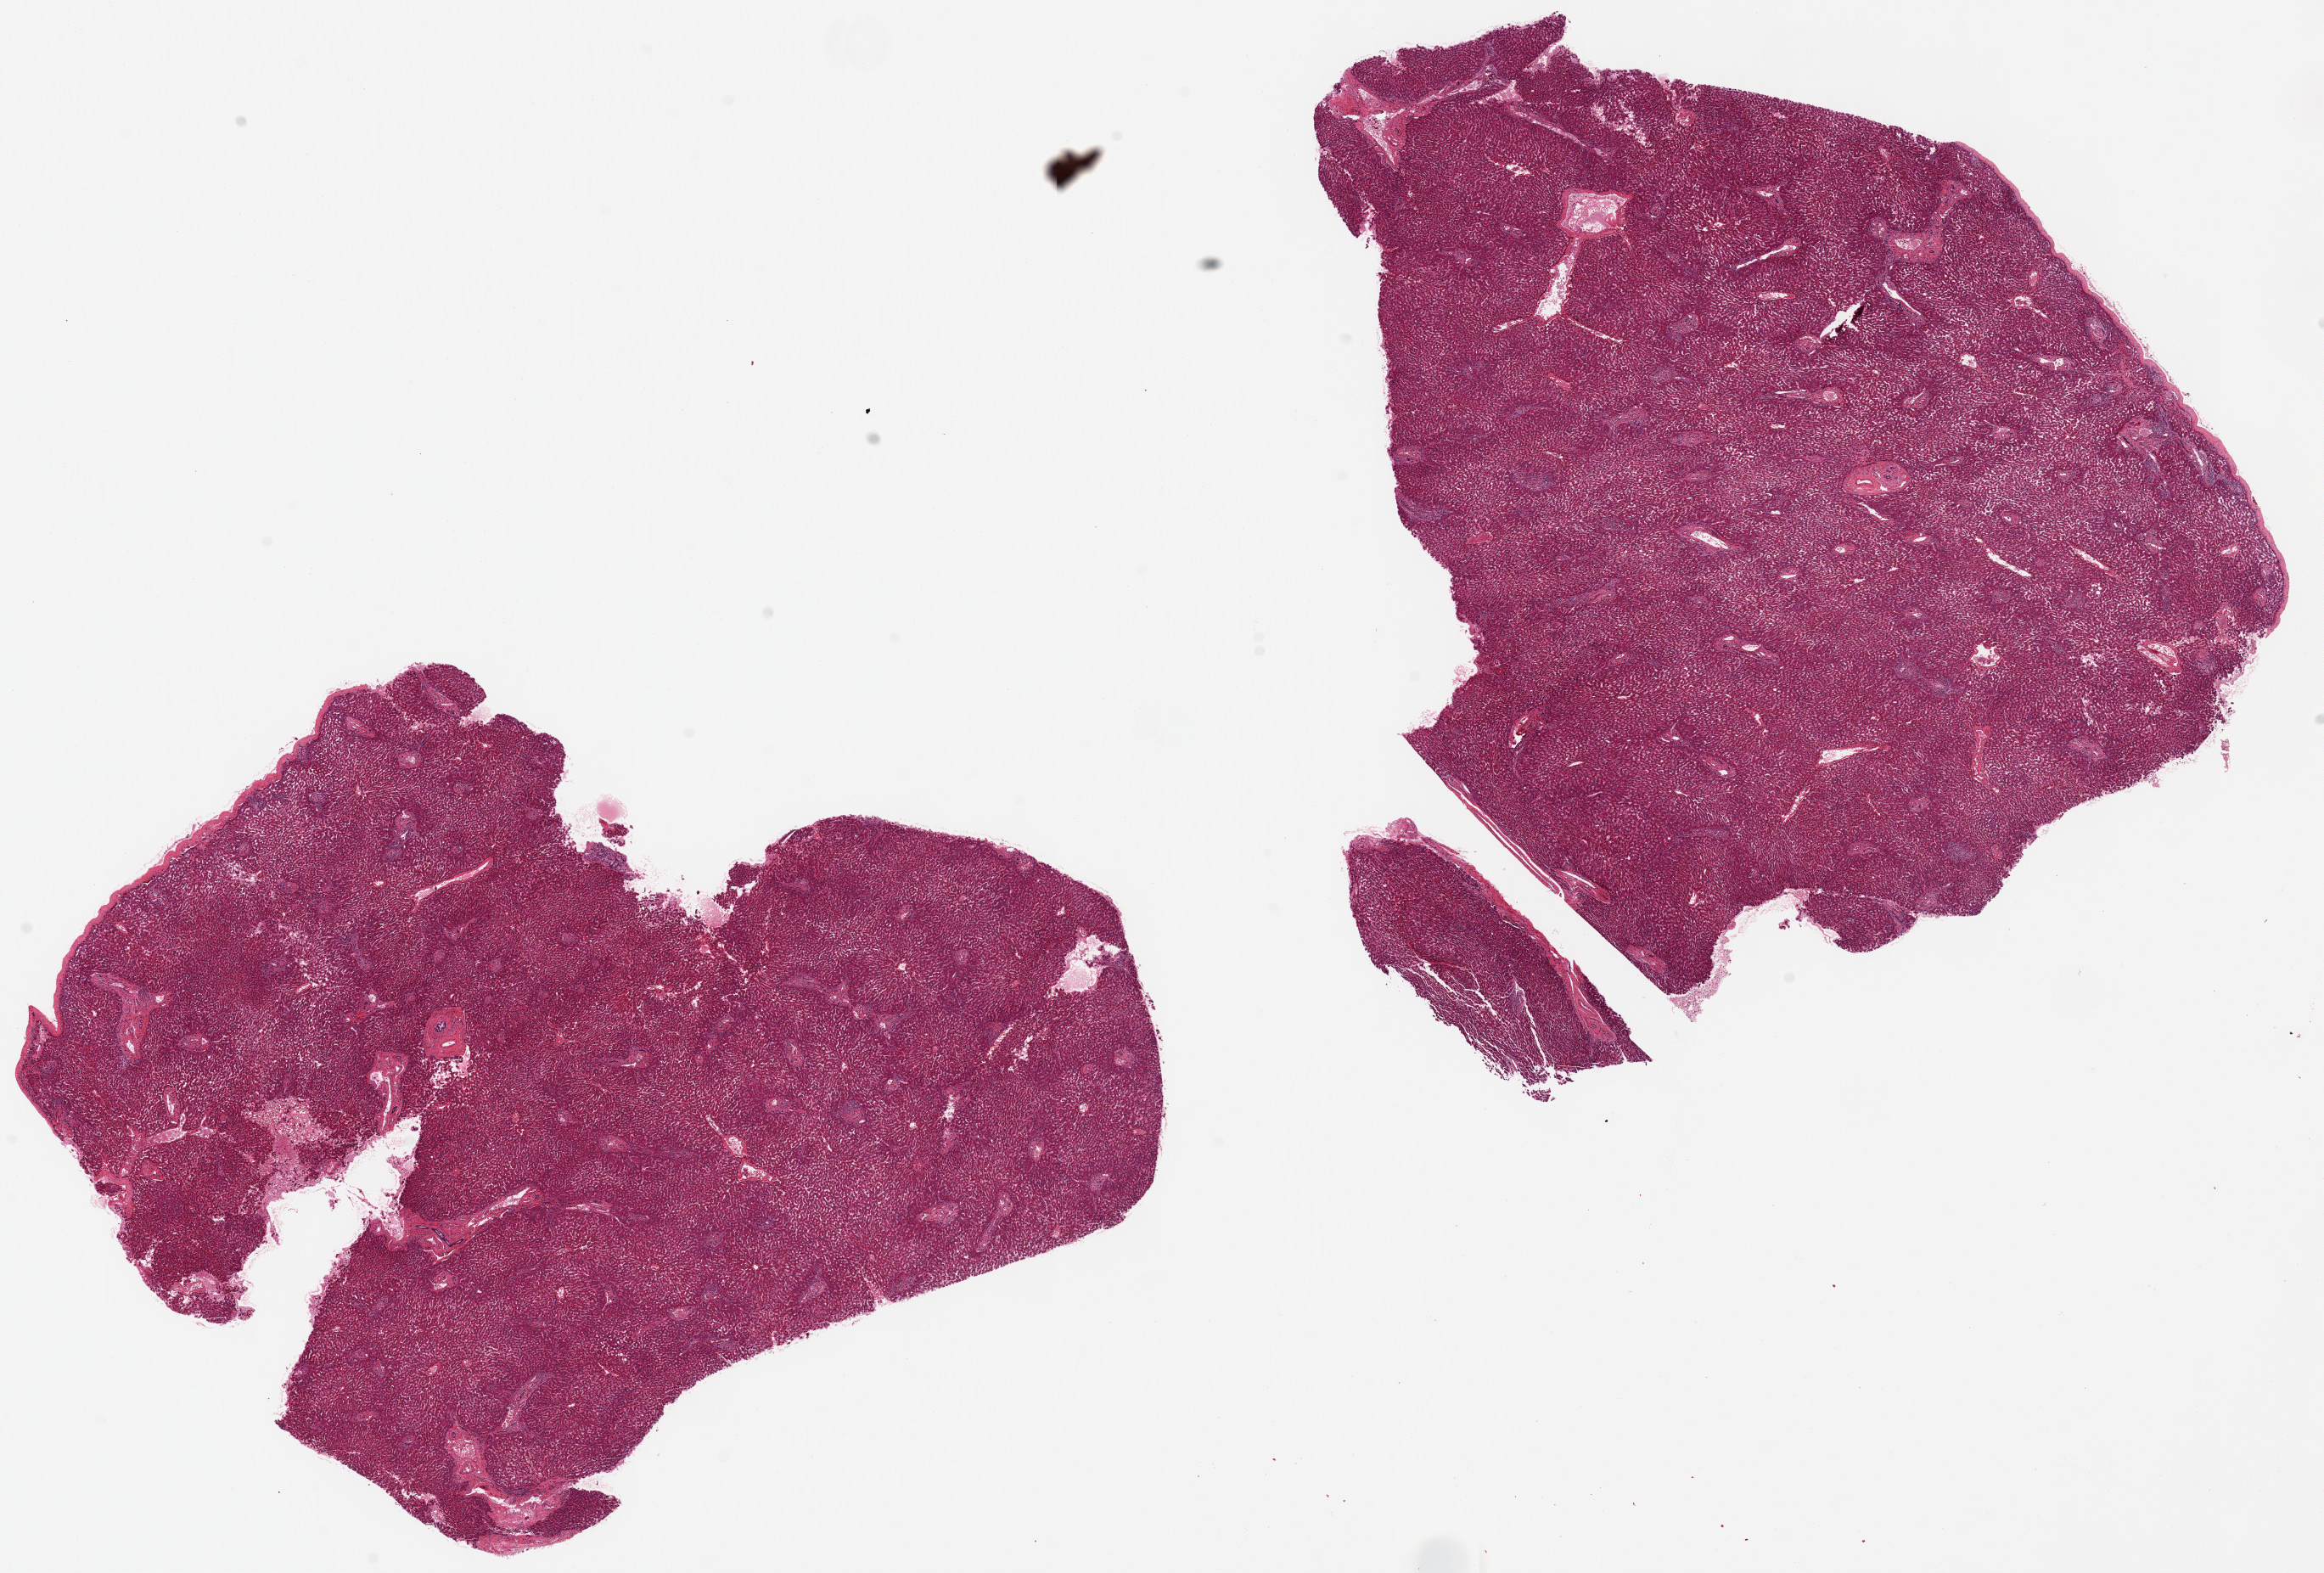
Haematoxylin and eosin whole-slide image, a low-resolution overview of the entire scanned area, about 21.7 x 14.7 mm (from a 20x scan); PAXgene-fixed paraffin-embedded (PFPE) section; sampled site (target tissue): liver; tissue donor sample. Donor sex: female.
- reviewer comment on this tissue sample: 2 pieces, 9x8 & 10x9mm; minimal fat/congestion